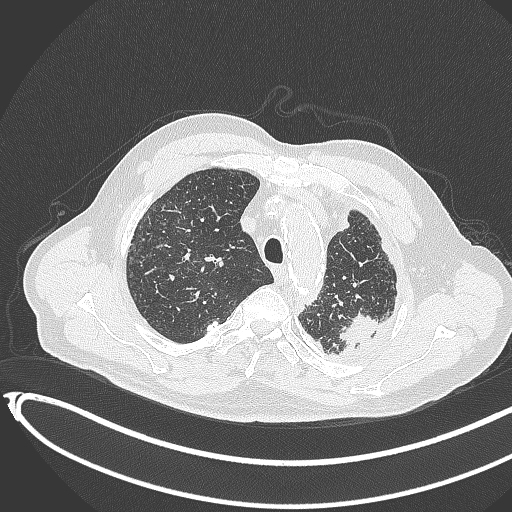
Chest CT, one axial slice. Slice 344 of 451 in the series (ordered by position). Lung window (W 1500 / L -600 HU). 1 mm slice thickness. 512 × 512 image matrix, field of view 400 × 400 mm. Male patient, age 78 years. Case-level facts recorded for this patient, not image findings: clinical TNM (as recorded): T1c N0 M1.
Outlined on this slice (rectangle marked by the reading radiologist):
- lung tumour (recorded histology: adenocarcinoma): bounding box (x1, y1, x2, y2) in pixels: (336, 311, 381, 347)